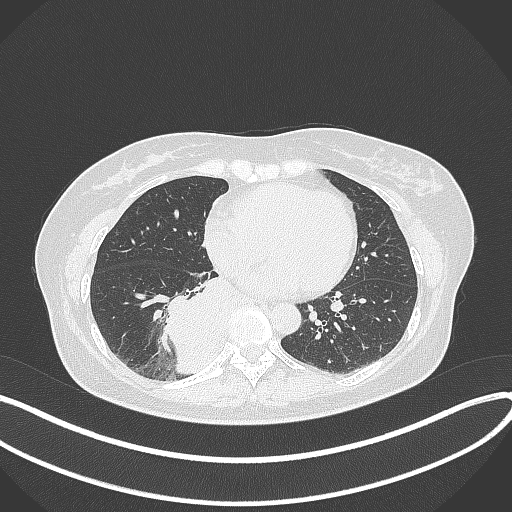
Chest CT, one axial slice; slice 136 of 331 in the series (ordered by position); 120 kVp; lung window (W 1500 / L -600 HU); 1 mm slice thickness; 512 × 512 image matrix, field of view 400 × 400 mm. Female patient, age 54 years. Case-level facts recorded for this patient, not image findings: clinical TNM (as recorded): T4 N0 M0.
Annotated regions visible in this slice (rectangle marked by the reading radiologist):
- lung tumour (recorded histology: adenocarcinoma): box from (x=164, y=275) to (x=233, y=373) px